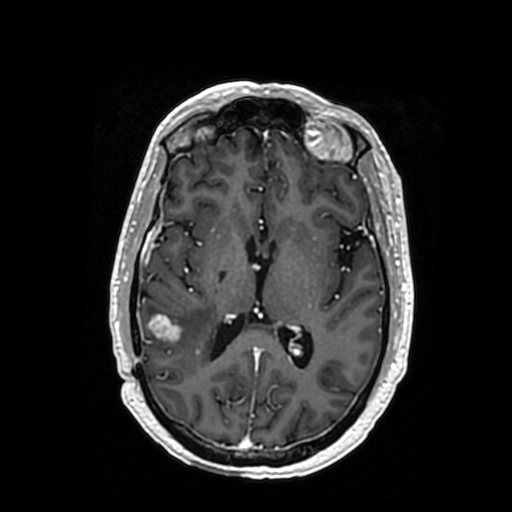
Brain MRI from a brain-tumour surgery series, one axial slice; position 177 of 364 along the scan axis; T1-weighted post-contrast; 0.5 mm slice thickness; 512 × 512 image matrix, field of view 260 × 260 mm. Case-level facts recorded for this patient, not image findings: histopathology: Oligodendroglioma; WHO grade: 3; IDH mutation: yes; tumour location: Right Posterior Temporal Inferior Parietal.
Outlined on this slice (expert manual segmentation):
- tumour: bounding box (x1, y1, x2, y2) in pixels: (146, 315, 217, 372)